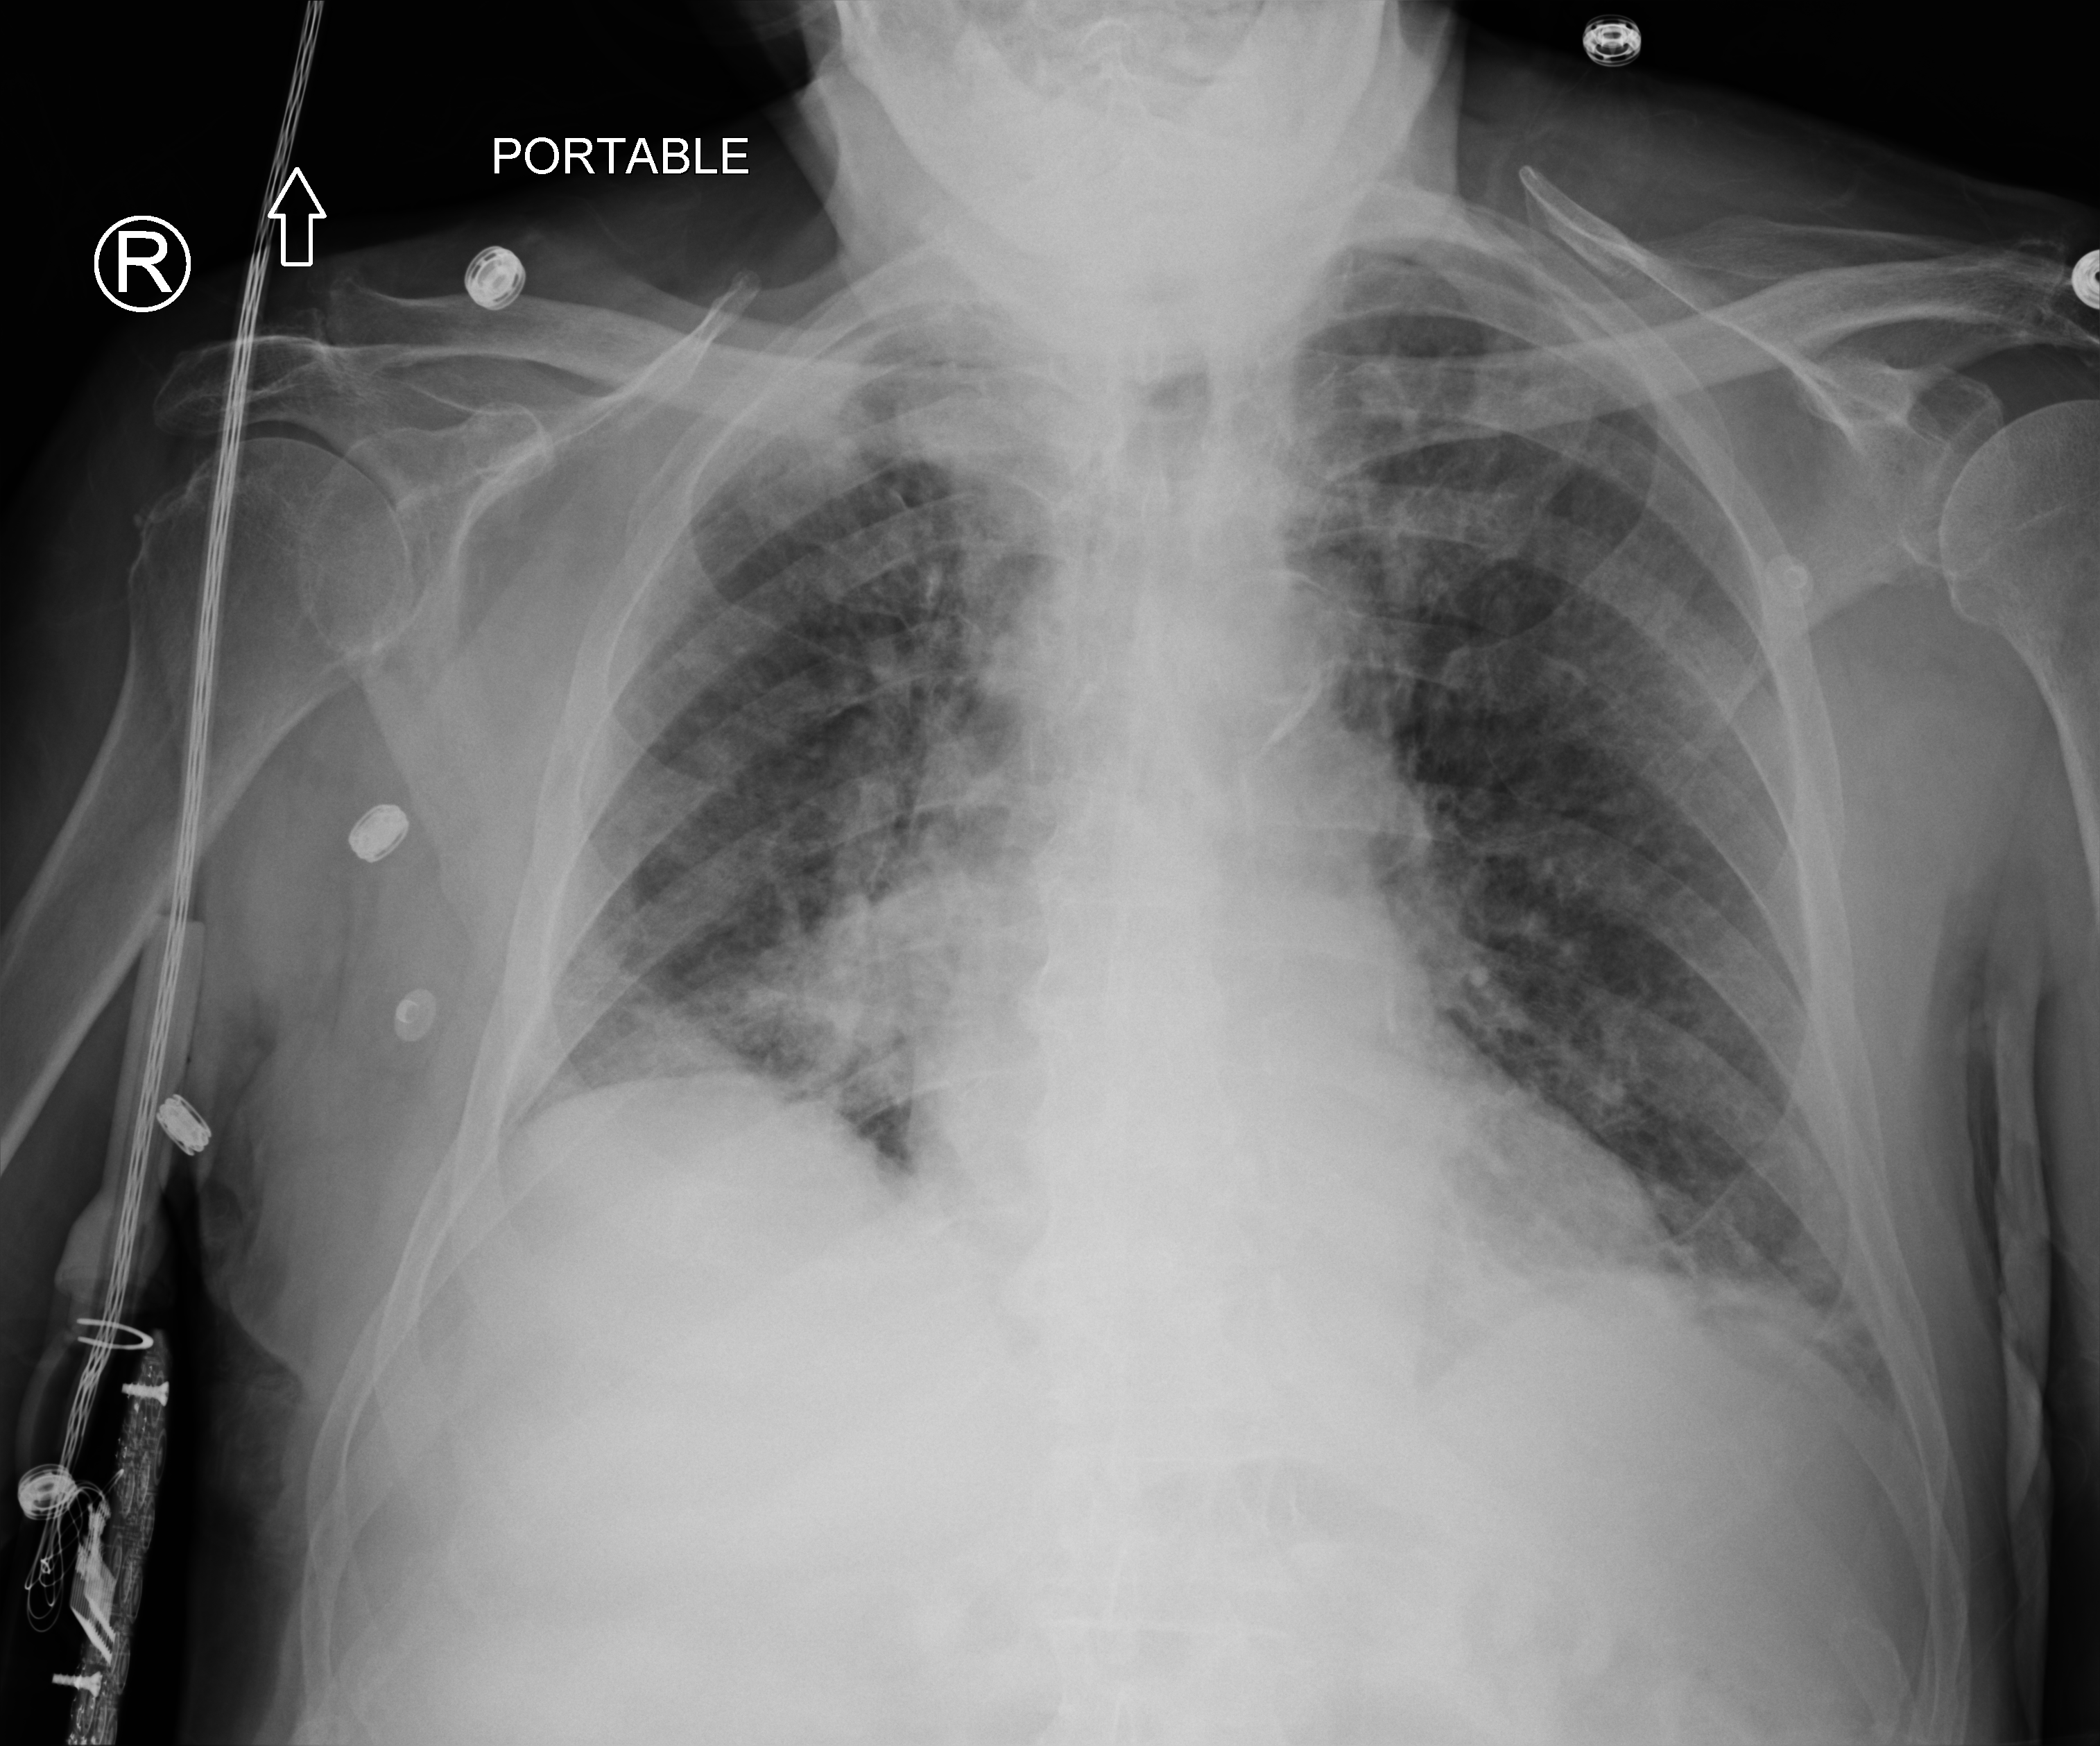
Portable chest radiograph; anteroposterior (AP) projection. Male patient hospitalised with COVID-19, age 75–90 years.
Hospital-stay facts (about this admission, not read from this image; timing relative to this image not recorded): admitted to intensive care during this hospital stay: yes; chronic kidney disease (admission record): no.